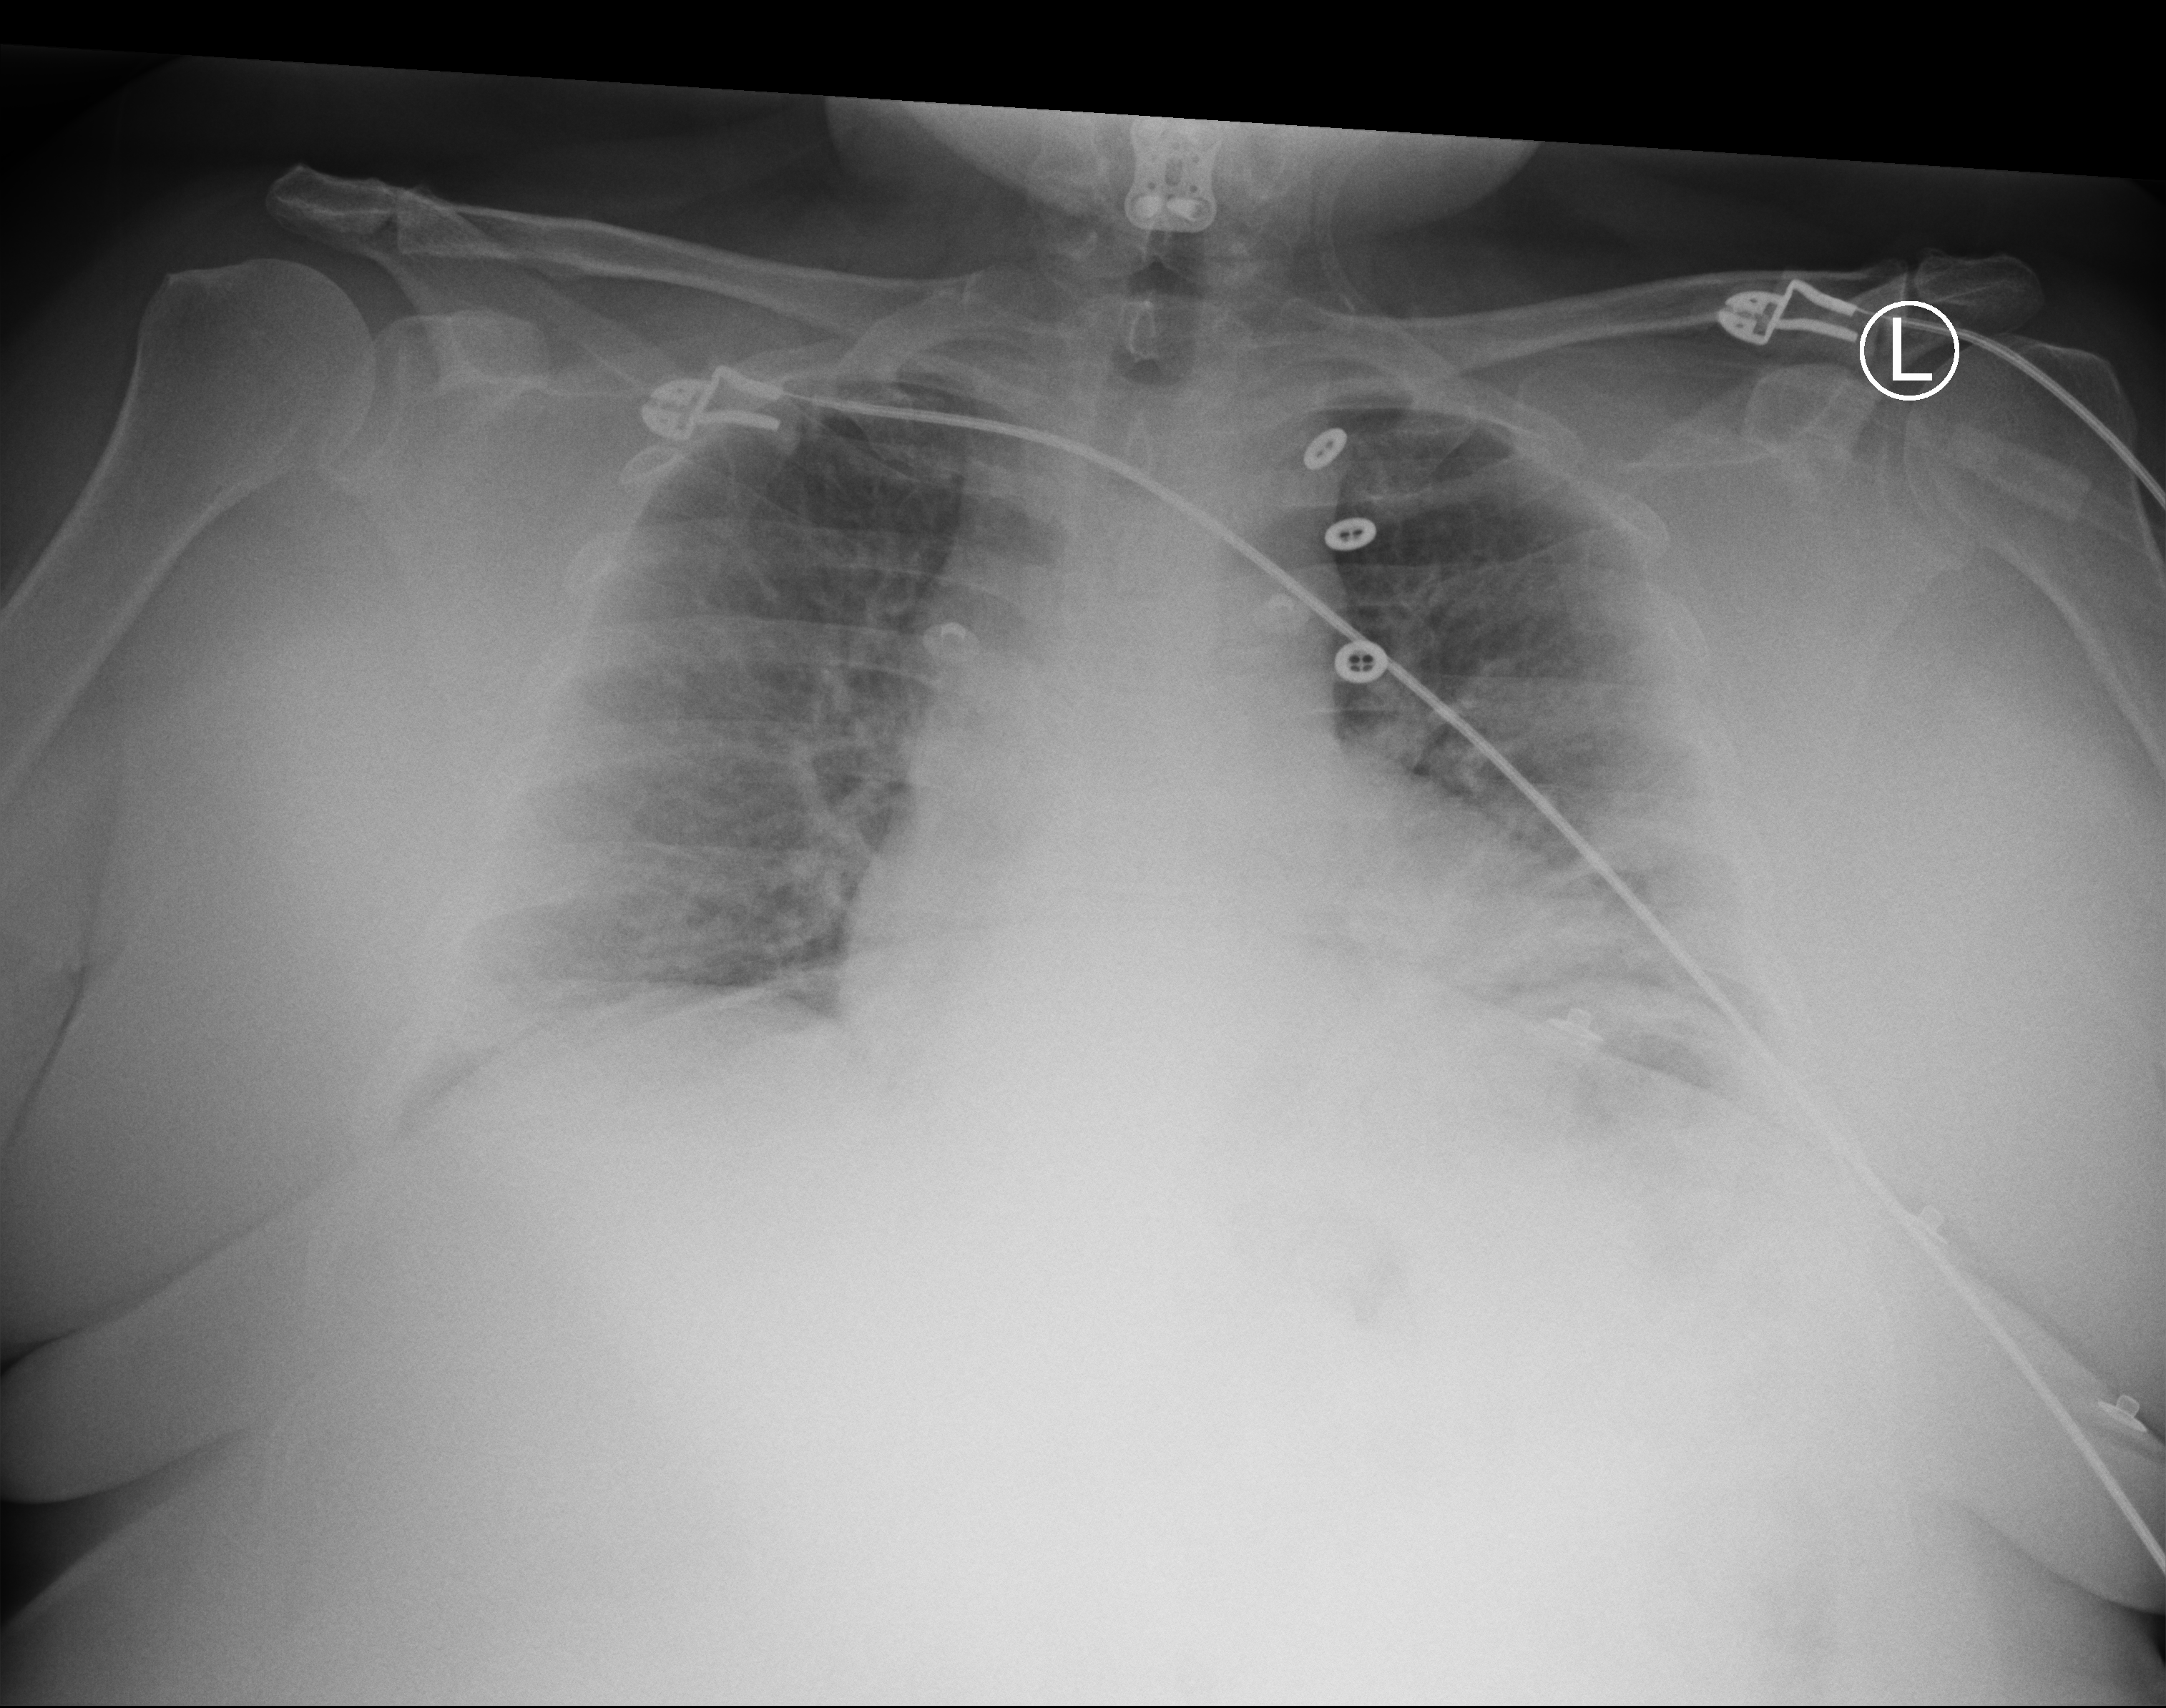
Portable chest radiograph. Female patient hospitalised with COVID-19, age 18–59 years.
Admission-level facts for this patient (not findings on this image; timing relative to this image not recorded): hypertension (admission record): yes.